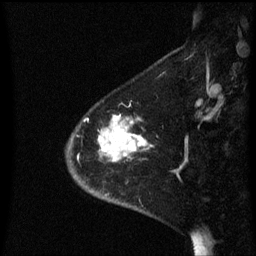
Breast MRI (dynamic contrast-enhanced), one sagittal slice. Position 17 of 60 along the scan axis. Dynamic contrast-enhanced series, image 2 of 3 at this slice position (ordered by acquisition). 1.5 T. TE 4.2 ms, TR 8.4 ms. 2.3 mm slice thickness. 256 × 256 image matrix, field of view 200 × 200 mm. Patient: female, 46 years. From the clinical record (not read from this slice): setting: breast cancer imaged before/during neoadjuvant chemotherapy; receptor status: HER2-positive.
Structures marked on this image (semi-automatically segmented with operator editing):
- analysis volume of interest (the breast-tissue region the enhancement analysis was run in; not a lesion): bounding box [x1, y1, x2, y2] px = [67, 116, 153, 187]
- tumour enhancement mask (voxels above the 70 % enhancement threshold inside the analysis volume of interest): [98, 116, 148, 163]